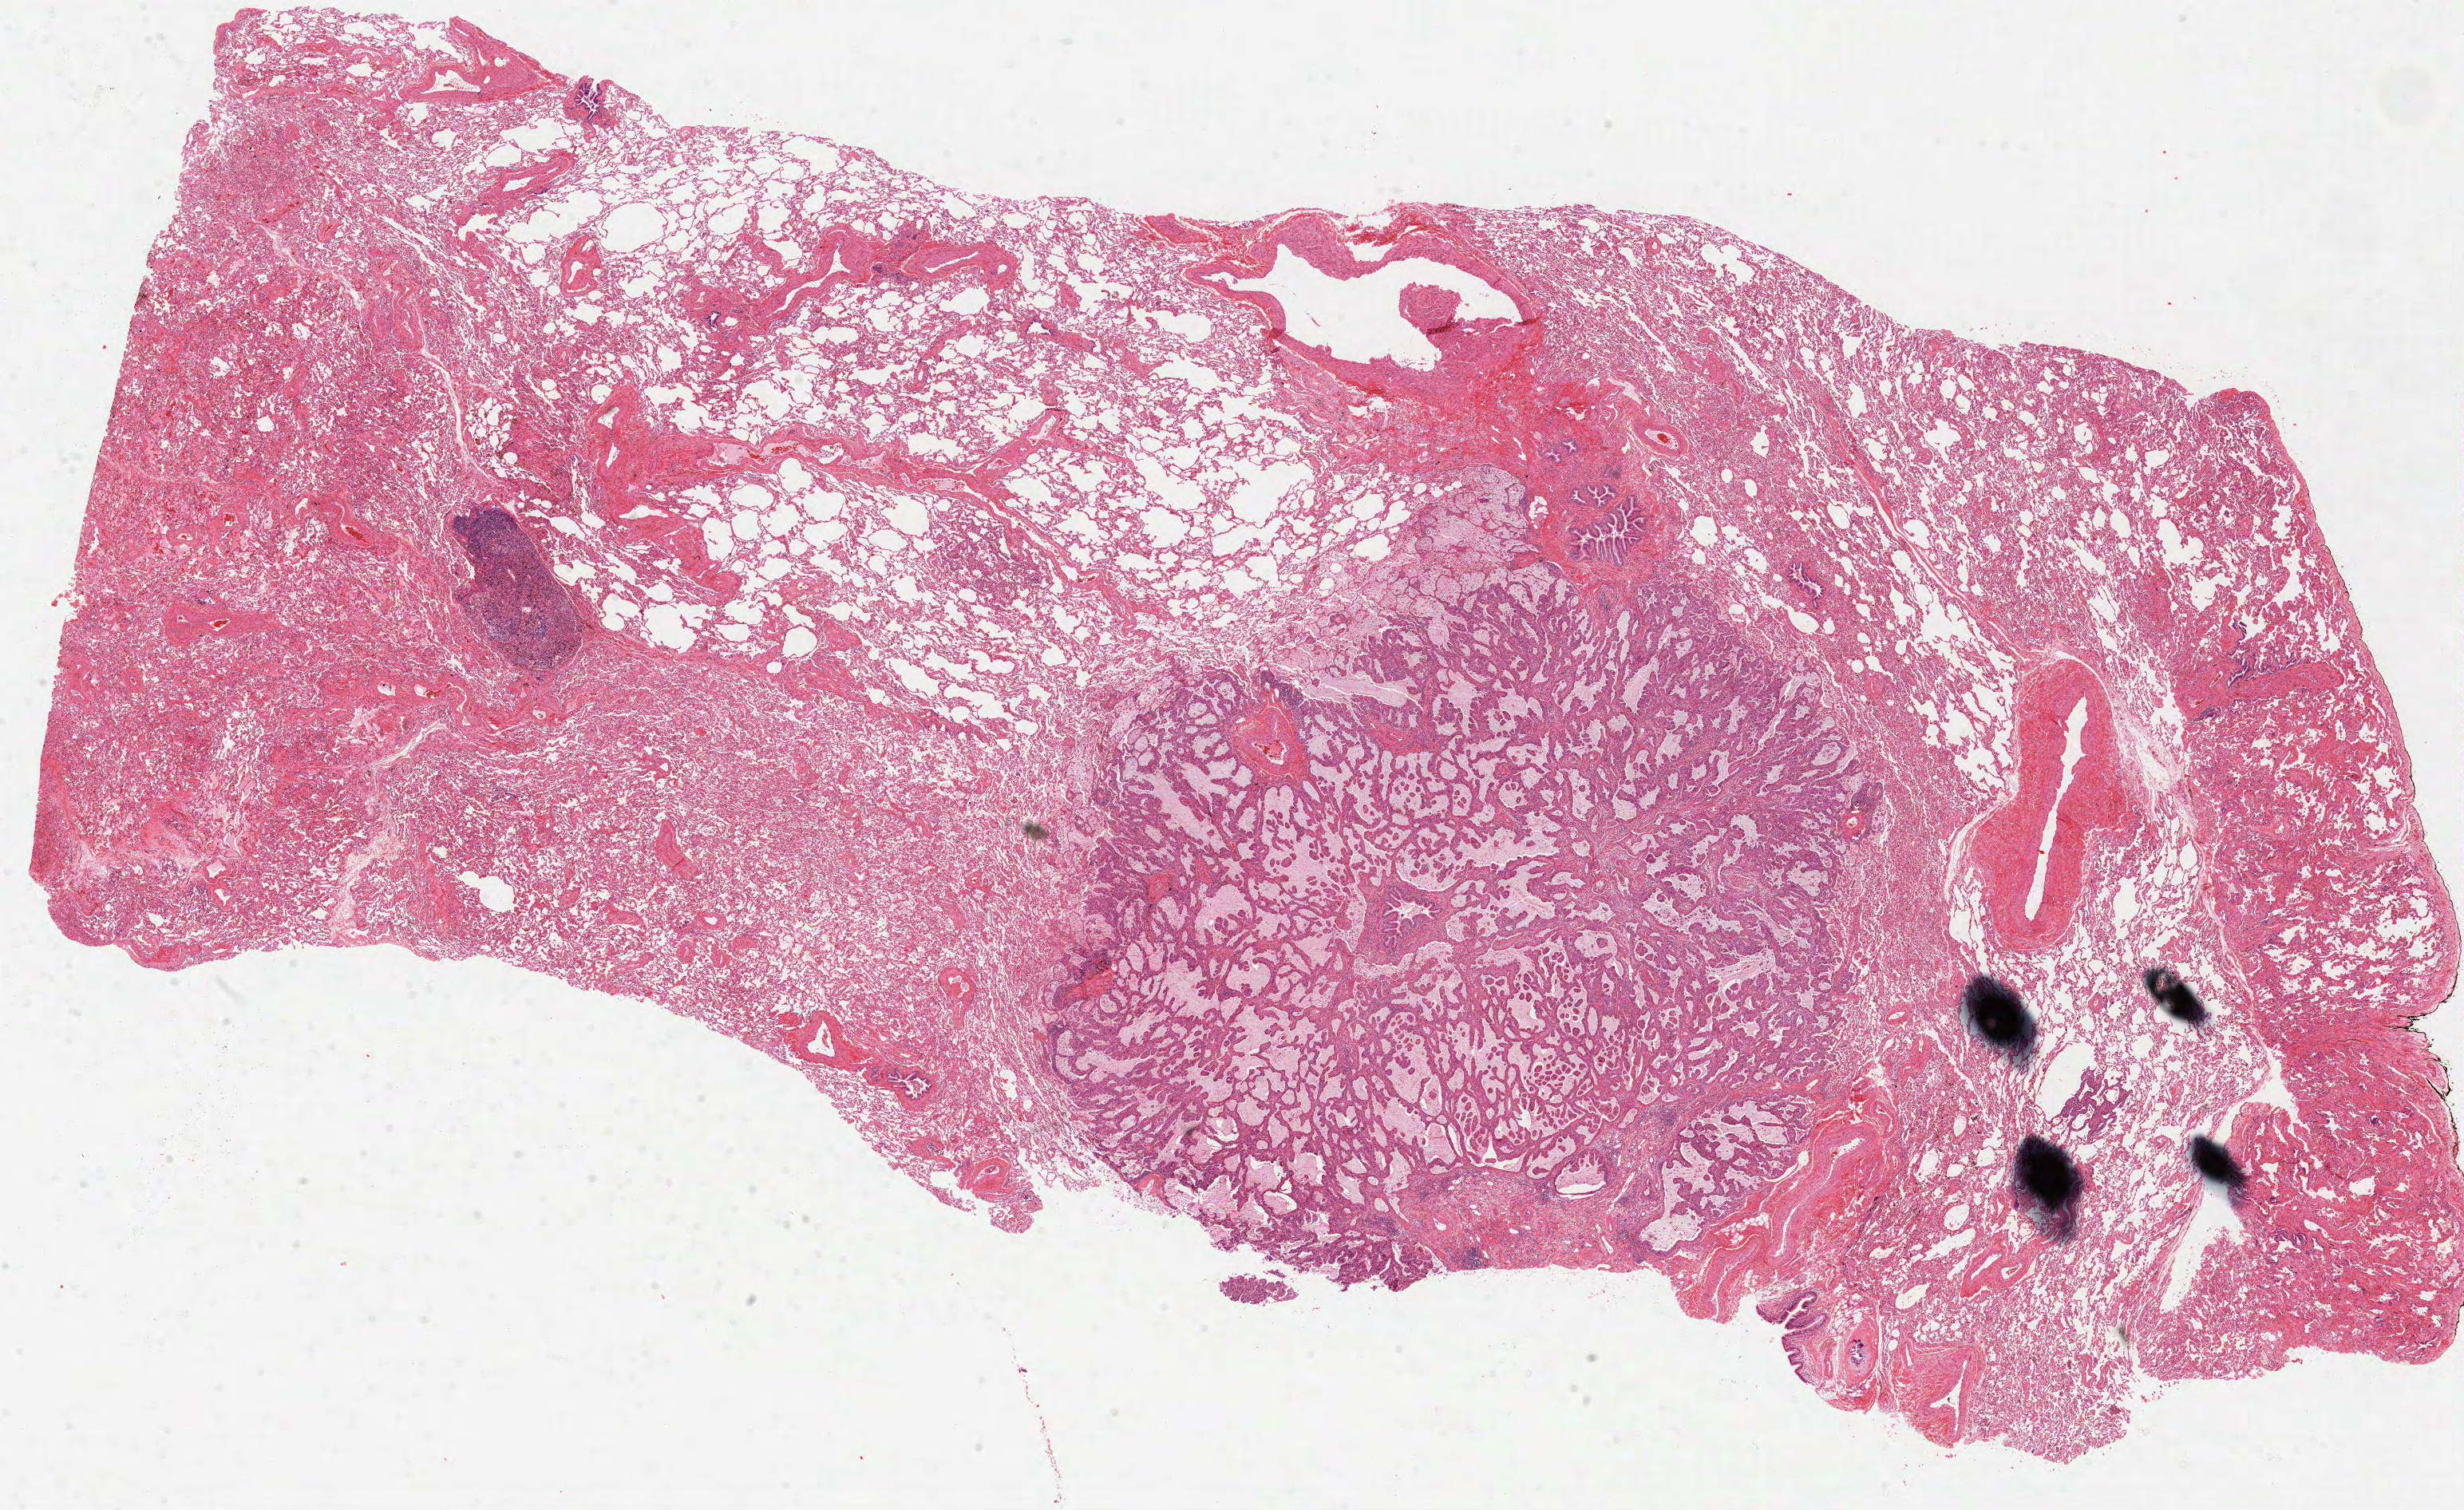
H&E-stained whole-slide image — whole scanned area (about 24.9 x 15.3 mm) shown as a low-resolution overview; FFPE section; sample: primary tumour, lung. Male, age 69 years at initial diagnosis.
AJCC pathologic stage: IA (7th edition). Laterality: right. Diagnosis: Acinar cell carcinoma (middle lobe, lung).